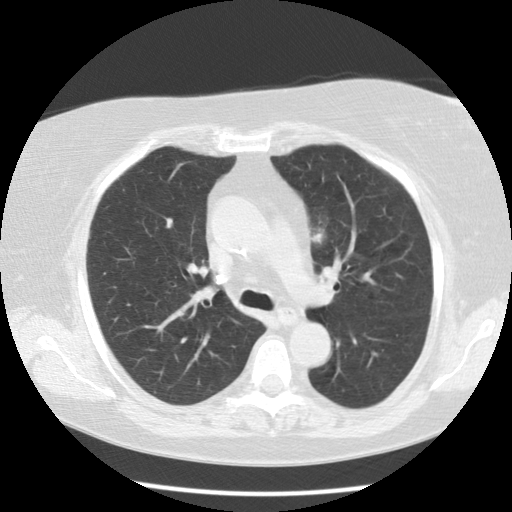
Axial slice from a low-dose chest CT screening exam. Second screening round (one year after baseline). Lung window (W 1500 / L -600 HU). 2.5 mm slice thickness. 120 kVp. Slice 33 of 109 in the series. 512 × 512 image matrix, field of view 334 × 334 mm. Female, age 67 years at enrolment.
- Lesion marked by an expert reader, bounding box [x1, y1, x2, y2] px = [292, 207, 352, 270].
- Reader record for this screening exam (exam-level; its link to the box is not recorded): non-calcified nodule or mass ≥4 mm, left upper lobe, 20 × 18 mm, poorly defined margins, soft tissue attenuation, pre-existing on the prior screen: yes; interval growth: yes.
- Later outcome: lung cancer diagnosed 28 days after this screen — adenocarcinoma, NOS, left upper lobe, moderately differentiated (G2), stage IIA (AJCC 6th edition), 23 mm at pathology.